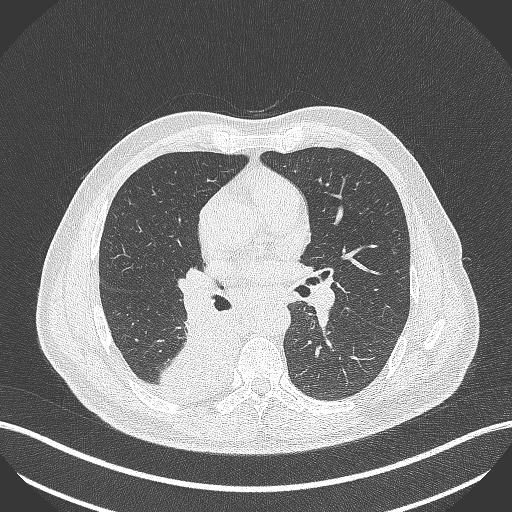
Chest CT, one axial slice. Position 257 of 451 along the scan axis. Reconstruction kernel B70f. Lung window (W 1500 / L -600 HU). 1 mm slice thickness. 512 × 512 image matrix, field of view 400 × 400 mm. Male patient, age 61 years. From the clinical record (not read from this slice): clinical TNM (as recorded): T1 N0 M0; histopathological grade: G3.
Annotated regions visible in this slice (rectangle marked by the reading radiologist):
- lung tumour (recorded histology: small cell carcinoma): box from (x=160, y=306) to (x=235, y=395) px